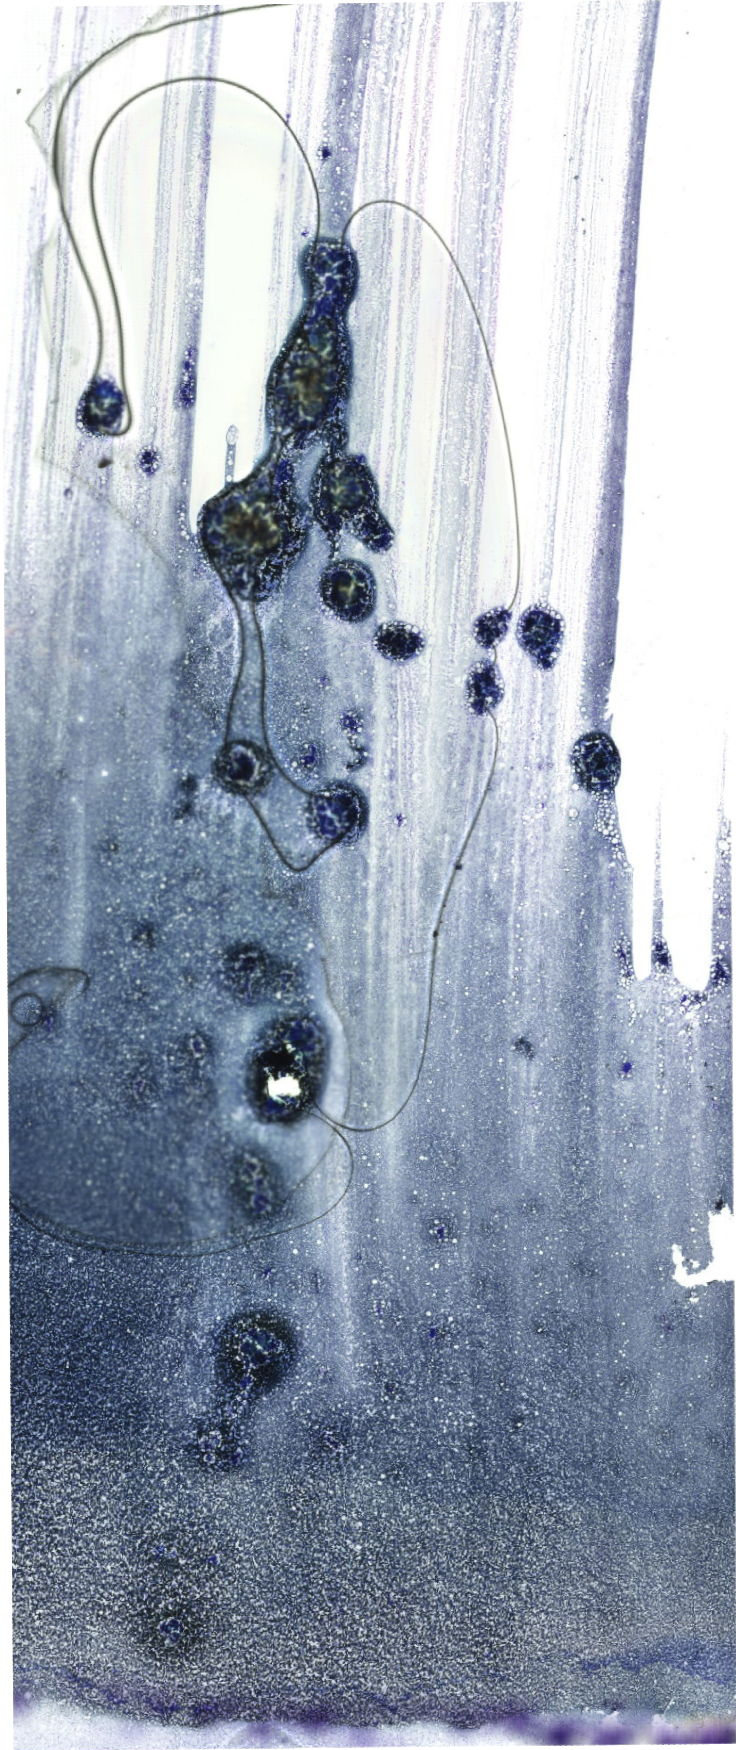
Whole-slide image of a May-Grünwald–Giemsa-stained bone marrow aspirate smear, low-resolution overview of the scanned area, about 20.9 x 49.6 mm. Male patient.
Diagnosis: Acute Myelomonocytic Leukemia.